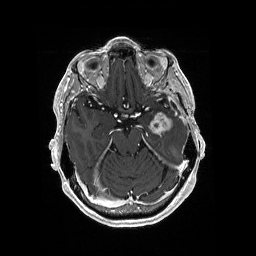
Brain MRI from a brain-tumour surgery series, one axial slice; slice 118 of 176 in the series (ordered by position); T1-weighted post-contrast; 1 mm slice thickness; 256 × 256 image matrix, field of view 256 × 256 mm. Case-level facts recorded for this patient, not image findings: histopathology: Glioblastoma; WHO grade: 4; IDH mutation: no; tumour location: Left Medial Temporal.
Structures marked on this image (expert manual segmentation):
- previous resection cavity: box from (x=173, y=105) to (x=176, y=108) px
- tumour: (x=148, y=112)–(x=174, y=136)